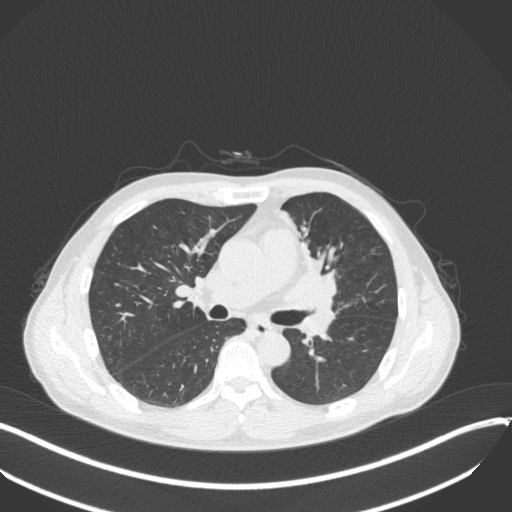
Chest CT, one axial slice. Slice 193 of 411 in the series (ordered by position). 120 kVp. Lung window (W 1500 / L -600 HU). 512 × 512 image matrix. Male patient, age 56 years. From the clinical record (not read from this slice): clinical TNM (as recorded): T2a N0 M0.
Structures marked on this image (rectangle marked by the reading radiologist):
- lung tumour (recorded histology: squamous cell carcinoma): bounding box [x1, y1, x2, y2] px = [282, 239, 338, 318]